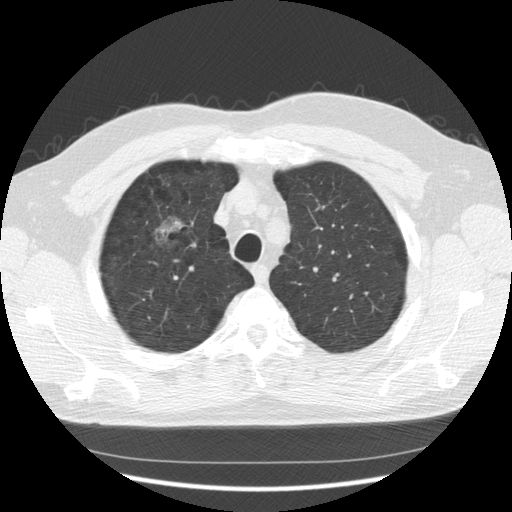
Low-dose screening chest CT, one axial slice; position 100 of 133 along the scan axis; reconstruction kernel STANDARD; 140 kVp; lung window (W 1500 / L -600 HU); 2.5 mm slice thickness; 512 × 512 image matrix, field of view 369 × 369 mm.
Structures marked on this image (outlined manually by an expert reader):
- lesion 1 (tumor, upper lobe of right lung): box from (x=156, y=218) to (x=184, y=240) px